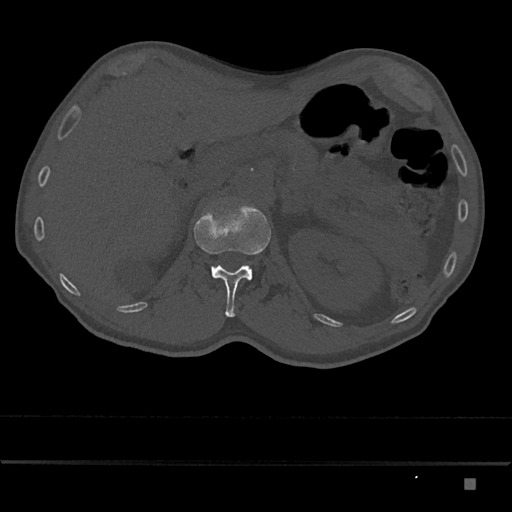
CT including the spine, one axial slice. Position 537 of 797 along the scan axis. 120 kVp. Bone window (W 1800 / L 400 HU). 0.5 mm slice thickness. 512 × 512 image matrix, field of view 390 × 390 mm. Male patient, age 72 years. Case-level facts recorded for this patient, not image findings: primary cancer: prostate.
Outlined on this slice (semi-automatic segmentation, software-assisted and operator-edited):
- L1 vertebra: bounding box [x1, y1, x2, y2] px = [194, 206, 271, 317]